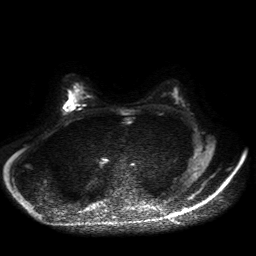
Breast MRI, one axial slice; position 28 of 50 along the scan axis; diffusion-weighted series; image 2 of 4 stored at this slice position (different b-values; order by instance number); 1.5 T; 4 mm slice thickness; 256 × 256 image matrix, field of view 360 × 360 mm. Female patient.
Outlined on this slice (outlined manually by an expert reader):
- tumour on diffusion-weighted imaging: bounding box (x1, y1, x2, y2) in pixels: (65, 101, 74, 111)